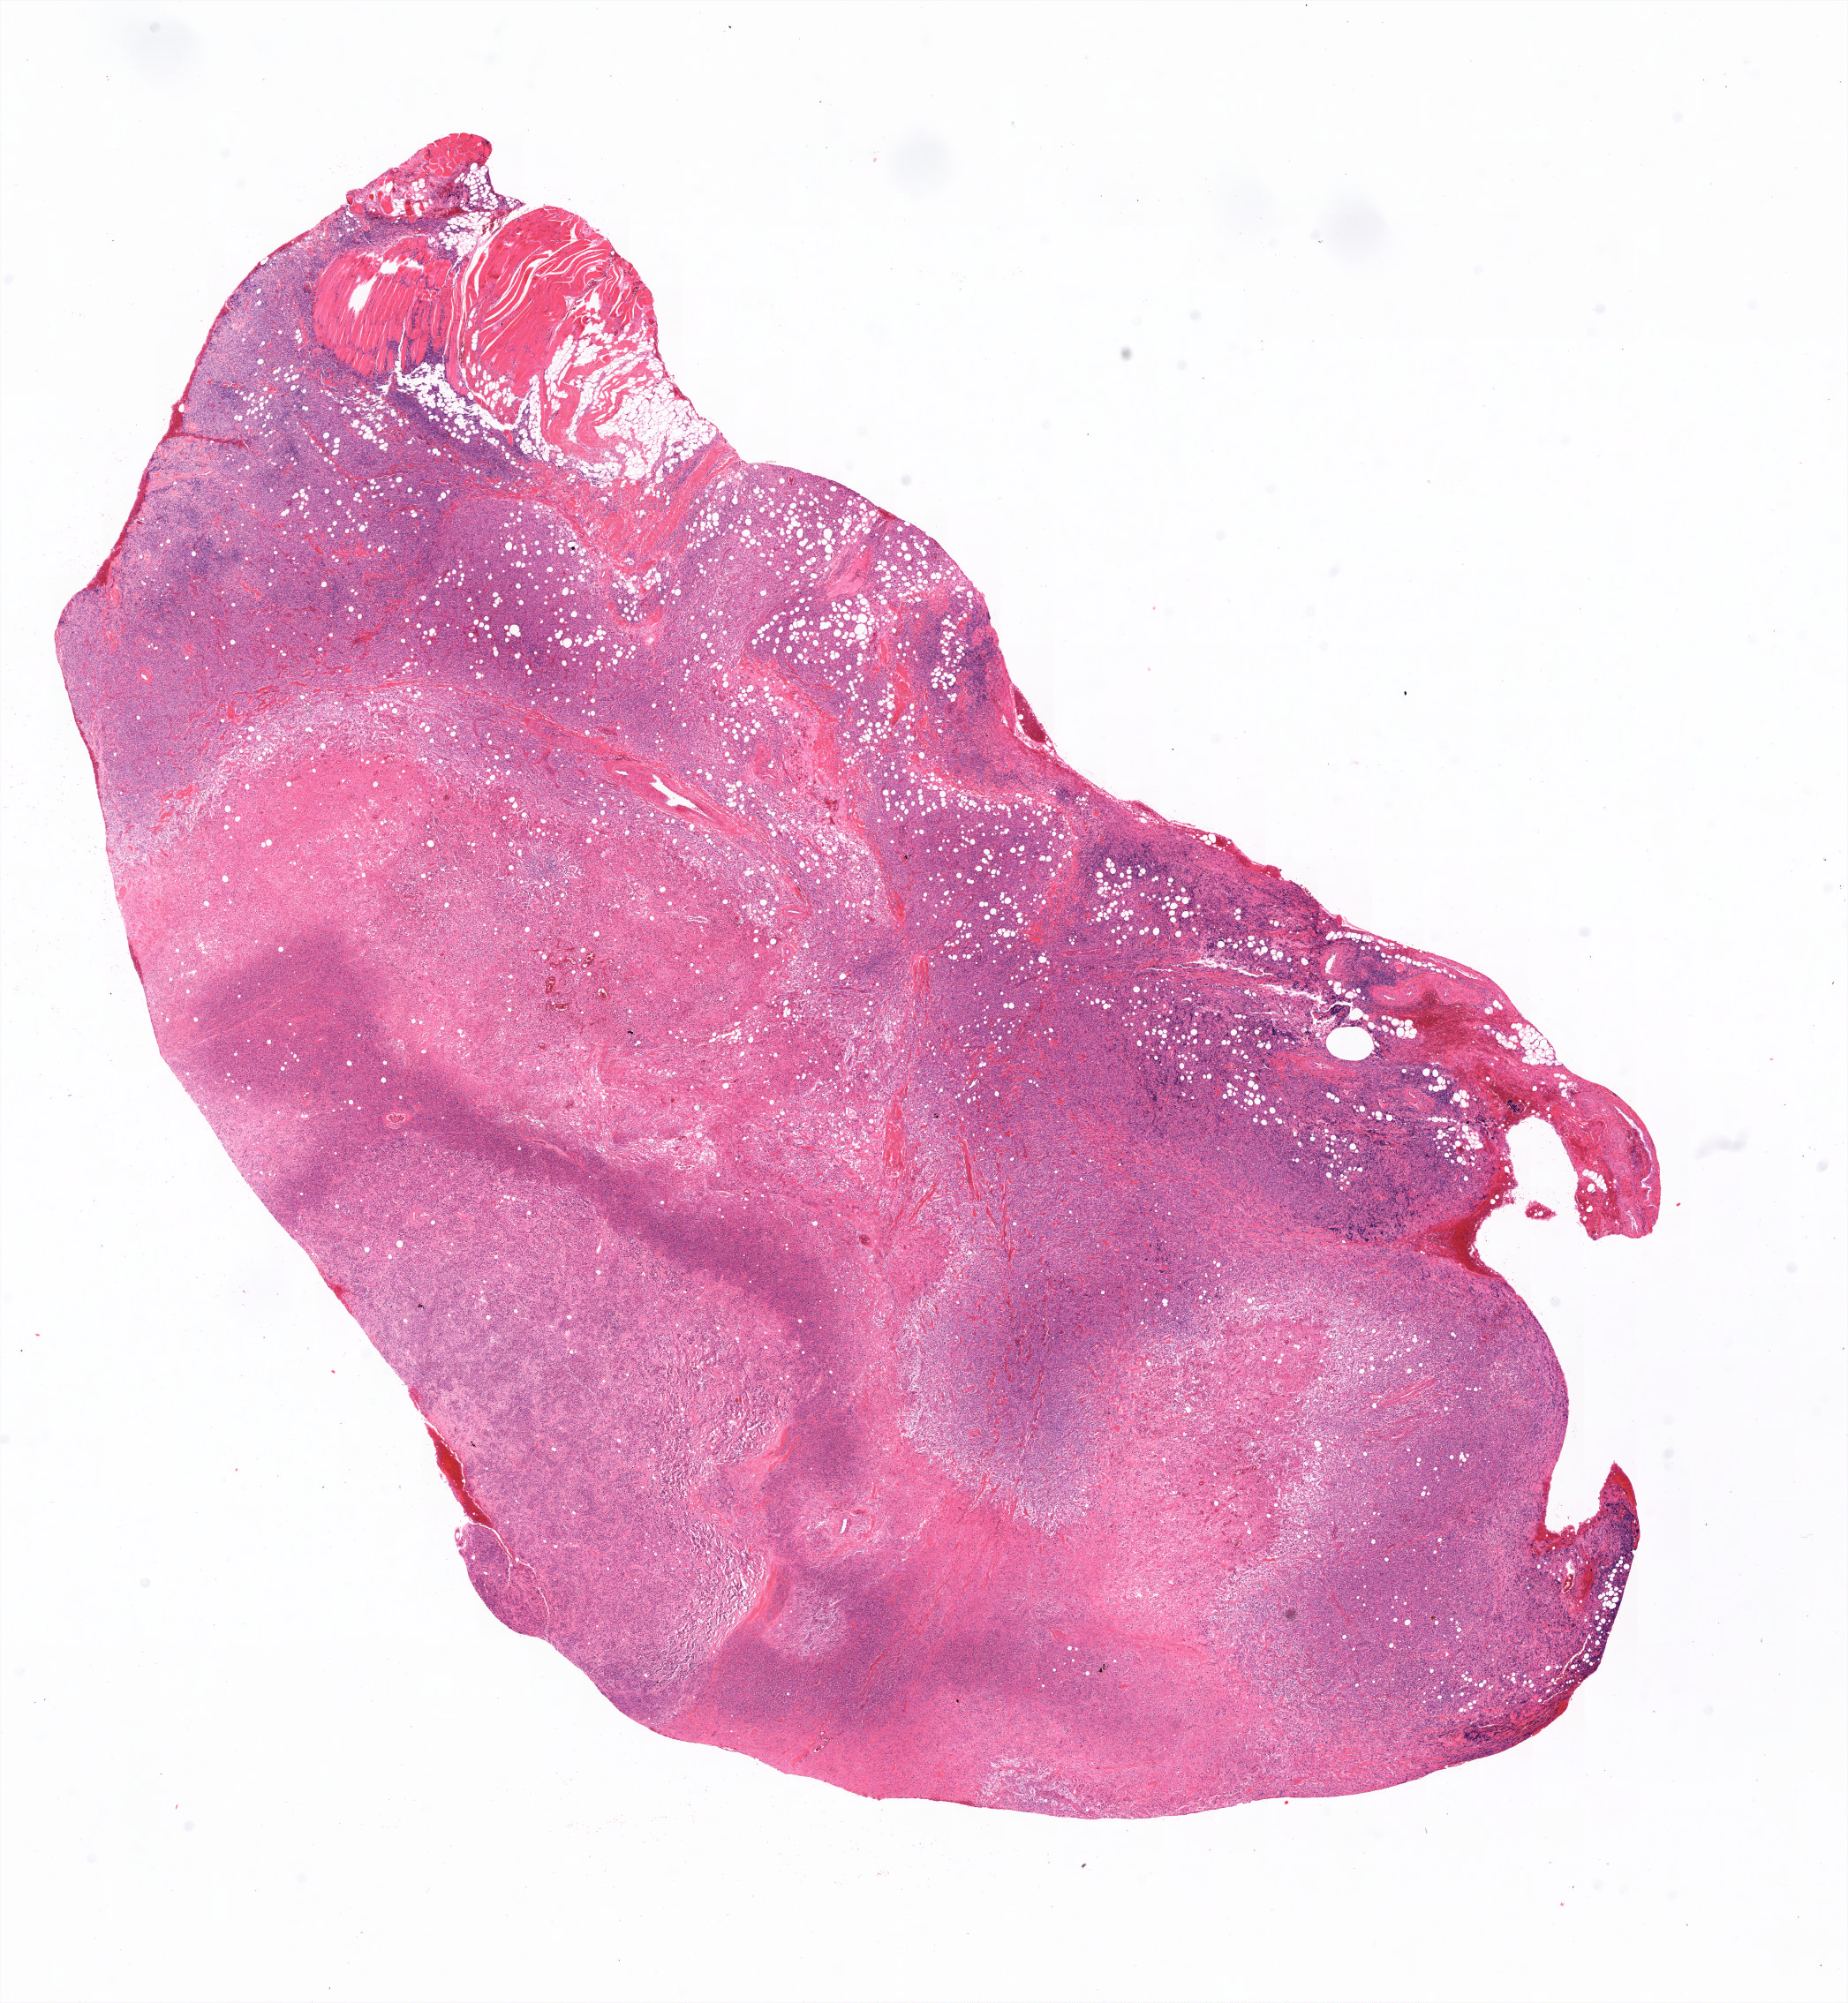
Whole-slide histology image, Hematoxylin and eosin (H&E) stained, a low-resolution overview of the entire scanned area, about 15.6 x 16.9 mm (slide scanned at 20x); formalin-fixed paraffin-embedded (FFPE) diagnostic section; lymphoid tissue, primary tumour sample. Patient: female, age at initial diagnosis 57 years.
- pathologic diagnosis: Diffuse large B-cell lymphoma, NOS (connective, subcutaneous and other soft tissues, NOS)